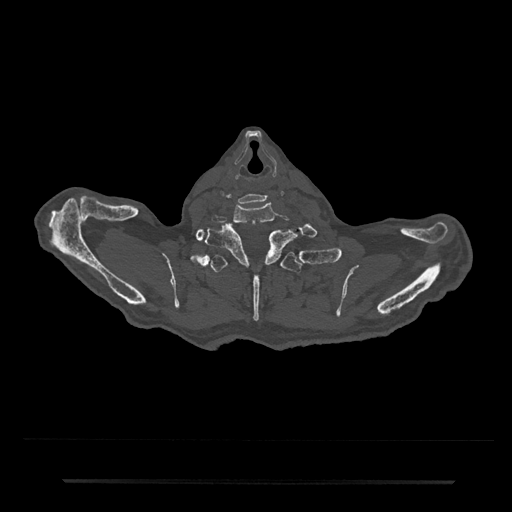
CT including the spine, one axial slice. Position 717 of 797 along the scan axis. Bone window (W 1800 / L 400 HU). 0.5 mm slice thickness. 512 × 512 image matrix, field of view 427 × 427 mm. Male patient, age 74 years. Case-level facts recorded for this patient, not image findings: primary cancer: prostate.
Annotated regions visible in this slice (semi-automatic segmentation, software-assisted and operator-edited):
- T1 vertebra: bounding box (x1, y1, x2, y2) in pixels: (206, 224, 296, 265)
- T2 vertebra: (200, 253, 313, 322)